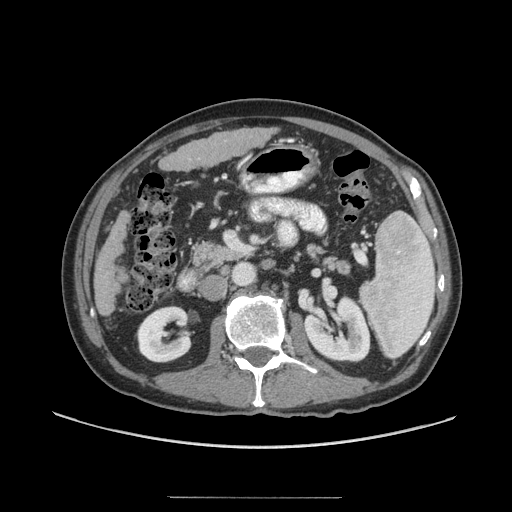
Contrast-enhanced abdominal CT (liver protocol), one axial slice. Position 16 of 71 along the scan axis. Reconstruction kernel STANDARD. 140 kVp. Soft-tissue window (W 400 / L 40 HU). 2.5 mm slice thickness. 512 × 512 image matrix, field of view 400 × 400 mm. Case-level facts recorded for this patient, not image findings: diagnosis: hepatocellular carcinoma (patient treated with transarterial chemoembolisation; whether this scan precedes or follows treatment is not stated here); TNM stage (as recorded): Stage-I; Child-Pugh class: A; tumour differentiation: well differentiated; tumour nodularity: uninodular.
Outlined on this slice (semi-automatically segmented with operator editing):
- liver parenchyma outside the tumour (the mass and vessels are separate outlines, so this box may not span the whole liver): bounding box <94,128,276,316> (left, top, right, bottom; pixels)